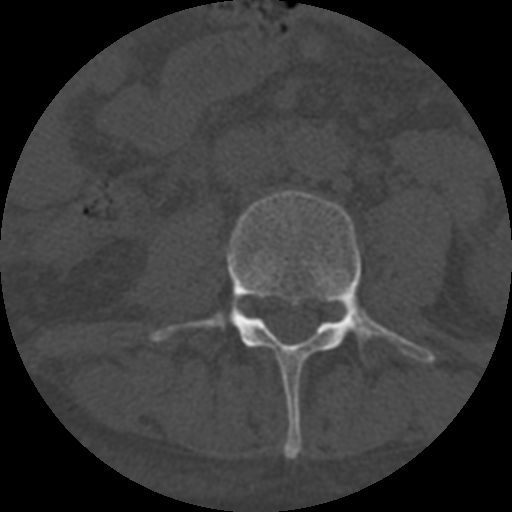
CT including the spine, one axial slice. Slice 232 of 708 in the series (ordered by position). Reconstruction kernel STANDARD. 120 kVp. One of 3 acquisitions stored at this slice position. Bone window (W 1800 / L 400 HU). 1.25 mm slice thickness. 512 × 512 image matrix, field of view 160 × 160 mm. Patient age 55 years. Case-level facts recorded for this patient, not image findings: primary cancer: colon; vertebrae with lytic lesions (as recorded): T12, L1, L5.
Annotated regions visible in this slice (semi-automatic segmentation, software-assisted and operator-edited):
- L3 vertebra: bounding box <151,190,435,459> (left, top, right, bottom; pixels)